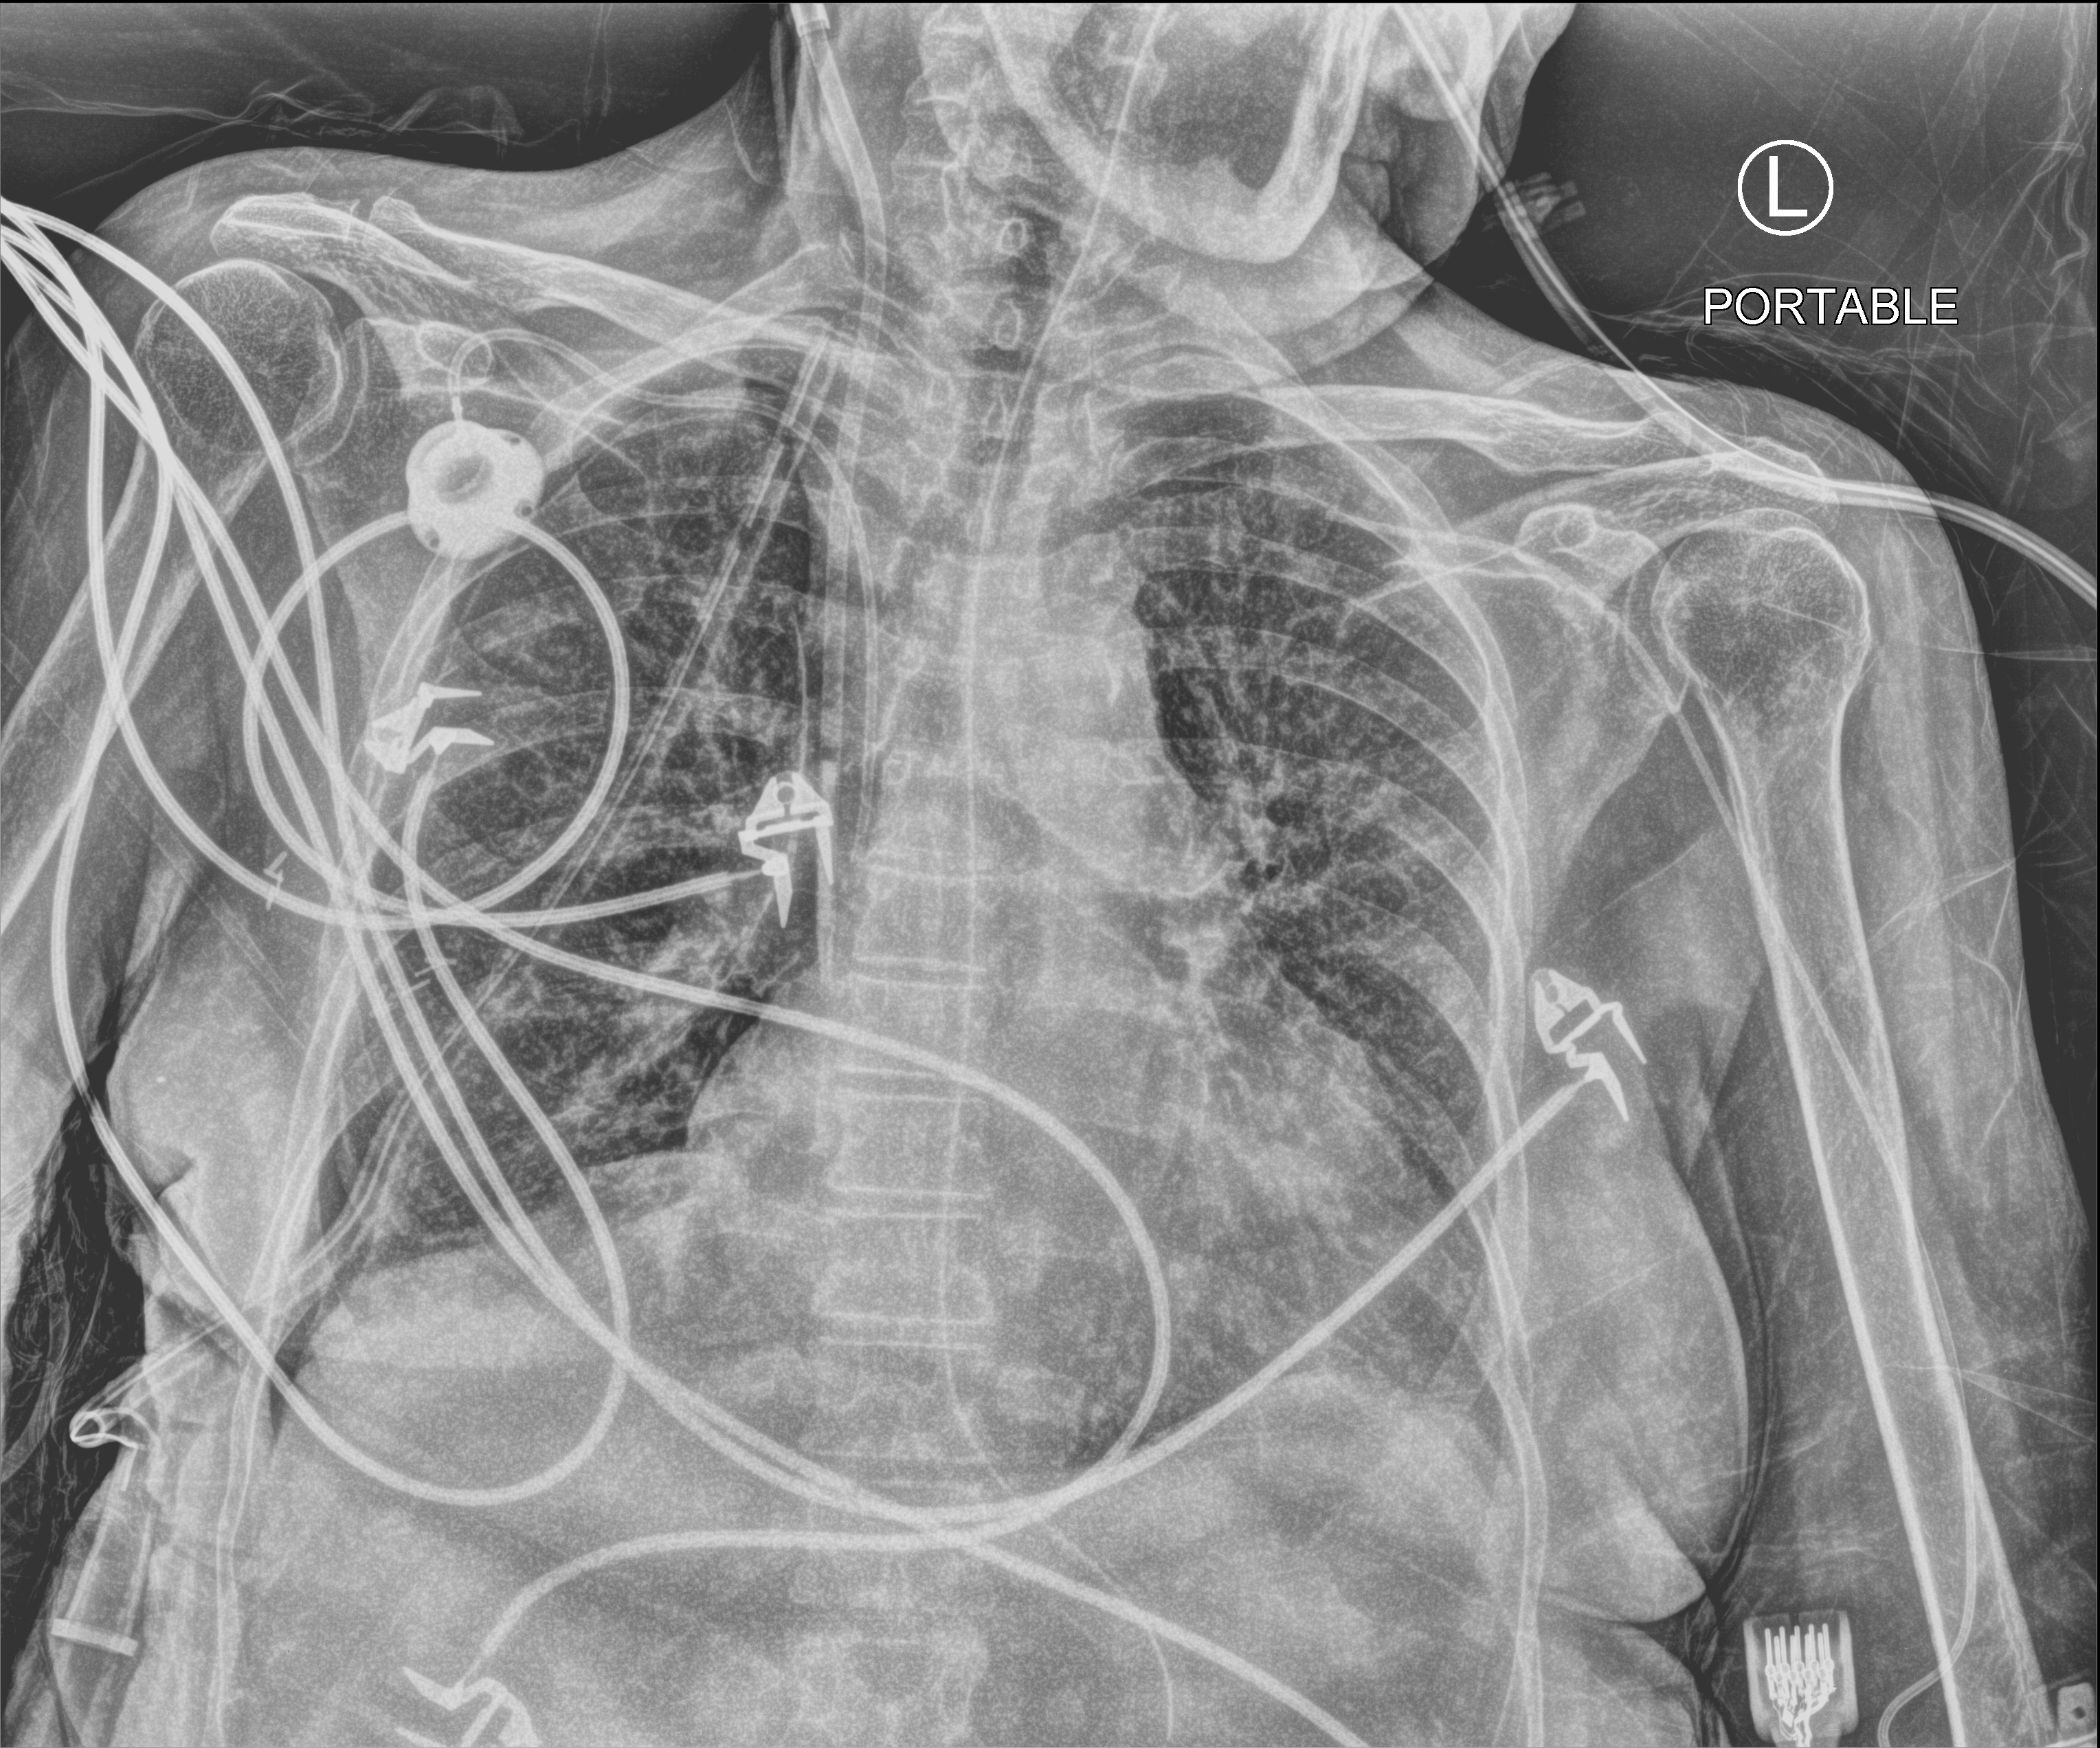
Bedside chest radiograph (computed radiography), anteroposterior (AP) projection. Female patient hospitalised with COVID-19, age 60–74 years.
From the hospital-stay record, not from the radiograph (when in the stay this image was taken is not recorded): chronic kidney disease (admission record): no; mechanically ventilated during this hospital stay: yes; admitted to intensive care during this hospital stay: yes.